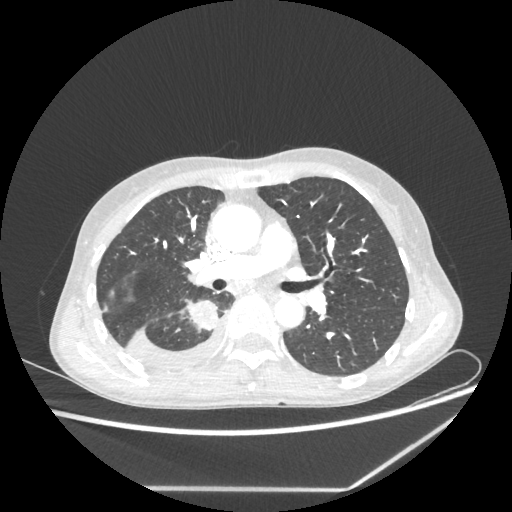
Chest CT, one axial slice; reconstruction kernel STANDARD; 80 kVp; lung window (W 1500 / L -600 HU); 512 × 512 image matrix, field of view 364 × 364 mm. Patient: female, 59 years. Case-level facts recorded for this patient, not image findings: clinical TNM (as recorded): T1c N1 M1.
Outlined on this slice (bounding box drawn by a radiologist):
- lung tumour (recorded histology: adenocarcinoma): bounding box [x1, y1, x2, y2] px = [185, 294, 219, 333]